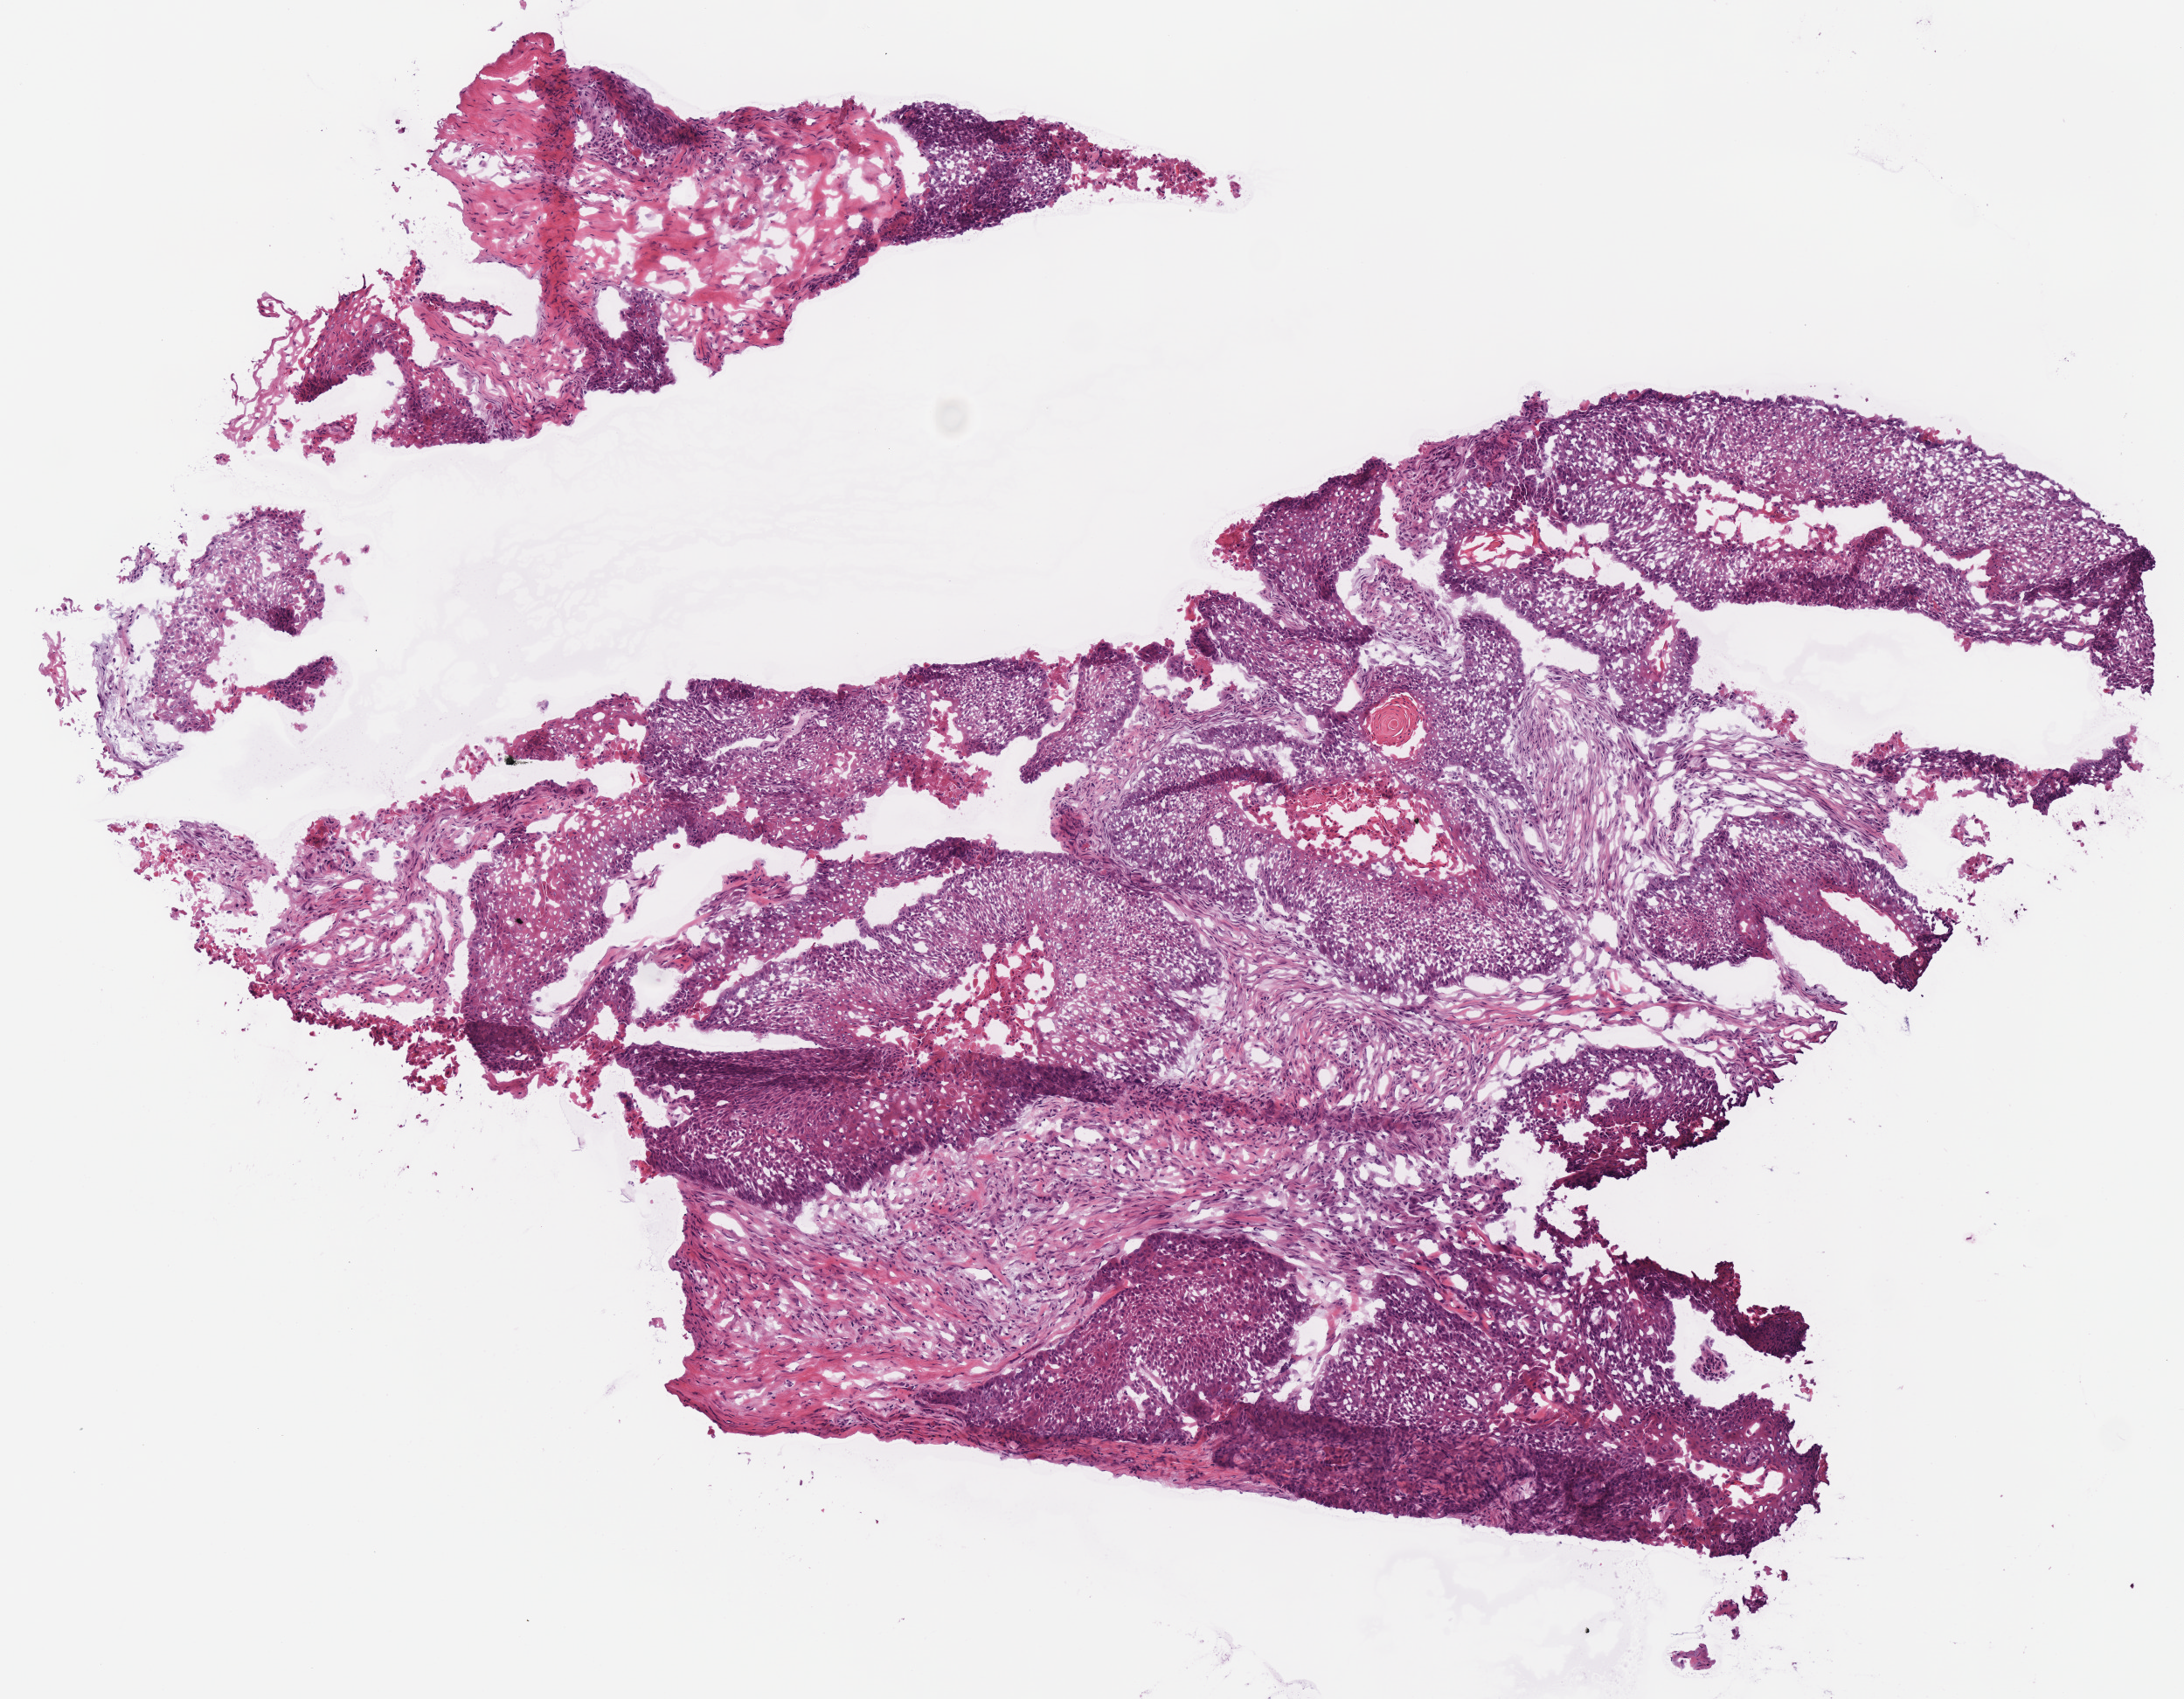
Whole-slide histology image, H&E — shown as a low-resolution overview of the whole scanned area (about 4.9 x 3.8 mm), frozen section, sample: primary tumour, head and neck. Patient: male, age at initial diagnosis 56 years. Histologic grade: G2 (moderately differentiated). Composition of this section per pathologist review: tumour cells 70%, tumour nuclei 70%, normal cells 0%, stromal cells 30%, necrosis 0%.
Diagnosis: Squamous cell carcinoma, NOS (larynx, NOS). AJCC pathologic stage: IVA (7th edition).